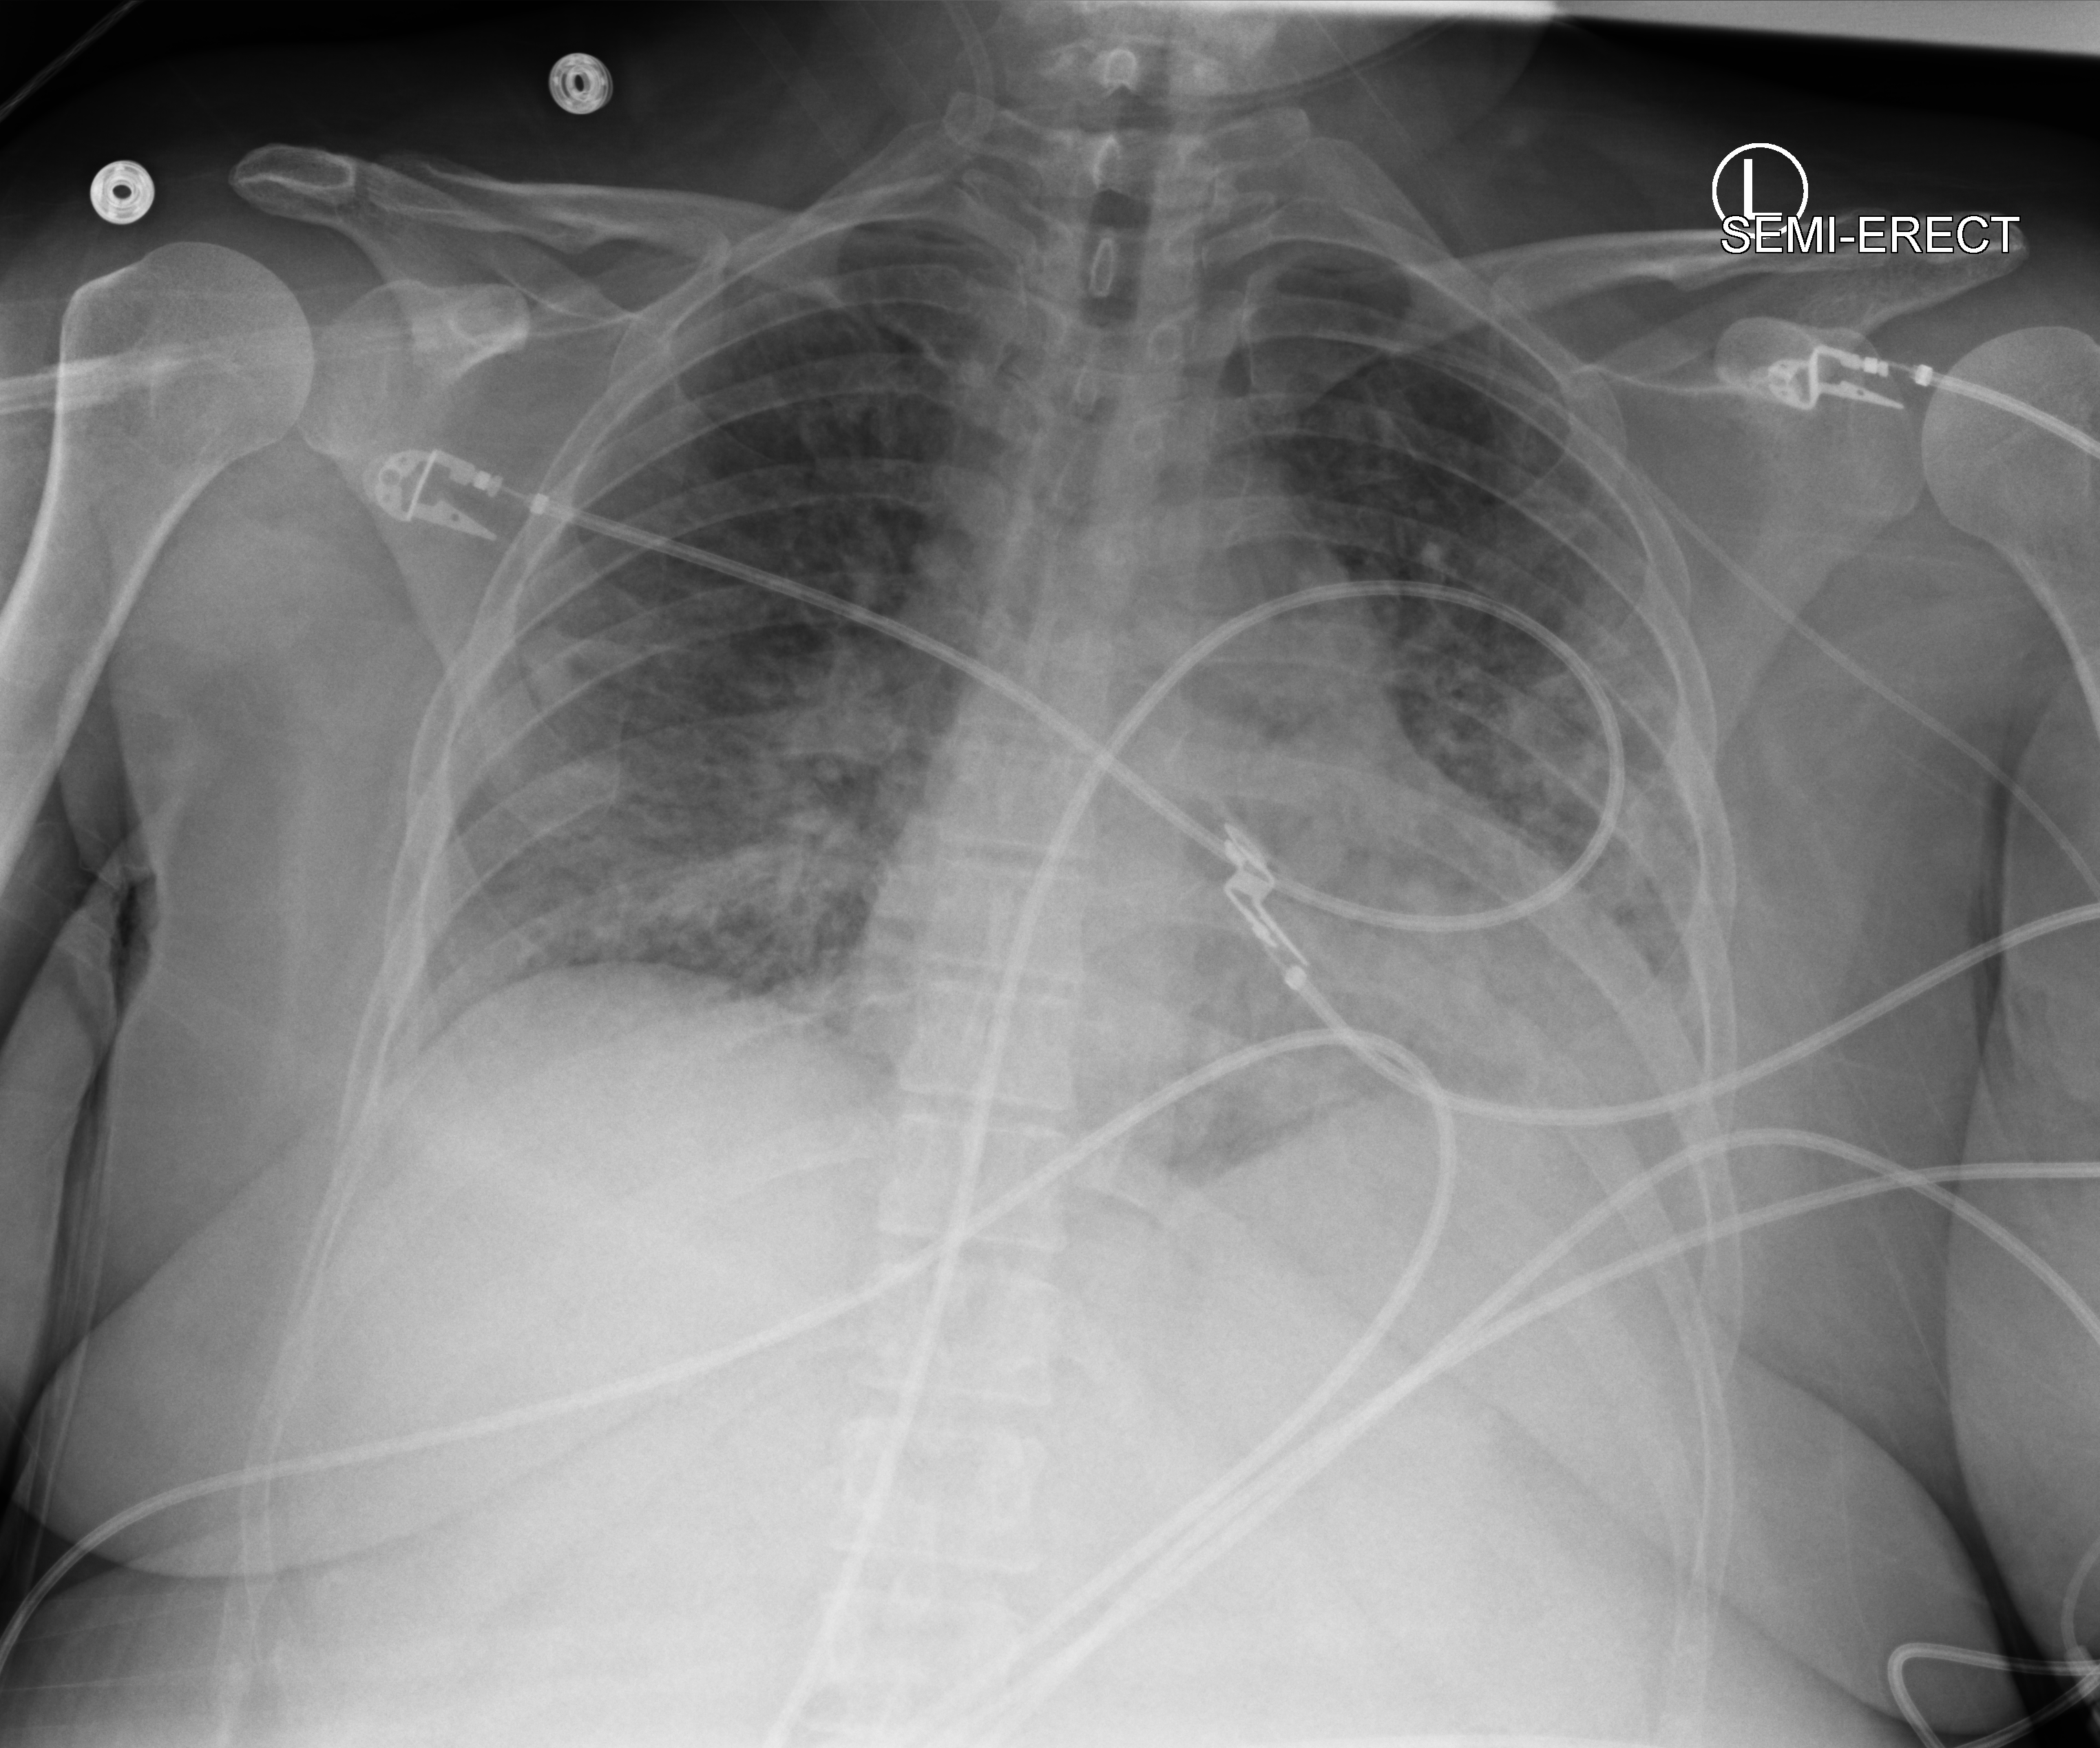
Chest X-ray (portable); anteroposterior (AP) projection. Female patient hospitalised with COVID-19, age 18–59 years.
Hospital-stay facts (about this admission, not read from this image; timing relative to this image not recorded): length of hospital stay: 31 days; mechanically ventilated during this hospital stay: yes.